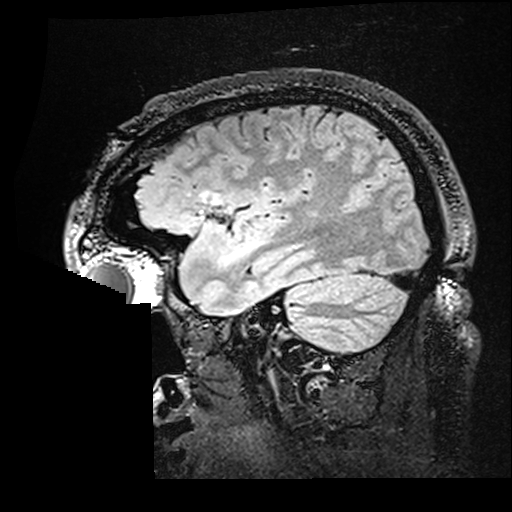
Brain MRI from a brain-tumour surgery series, one sagittal slice; slice 127 of 176 in the series (ordered by position); T2 FLAIR; 1 mm slice thickness; 512 × 512 image matrix, field of view 250 × 250 mm. Case-level facts recorded for this patient, not image findings: histopathology: Astrocytoma; WHO grade: 2; IDH mutation: yes.
Structures marked on this image (manually delineated by an expert):
- residual tumour: box from (x=204, y=195) to (x=257, y=256) px